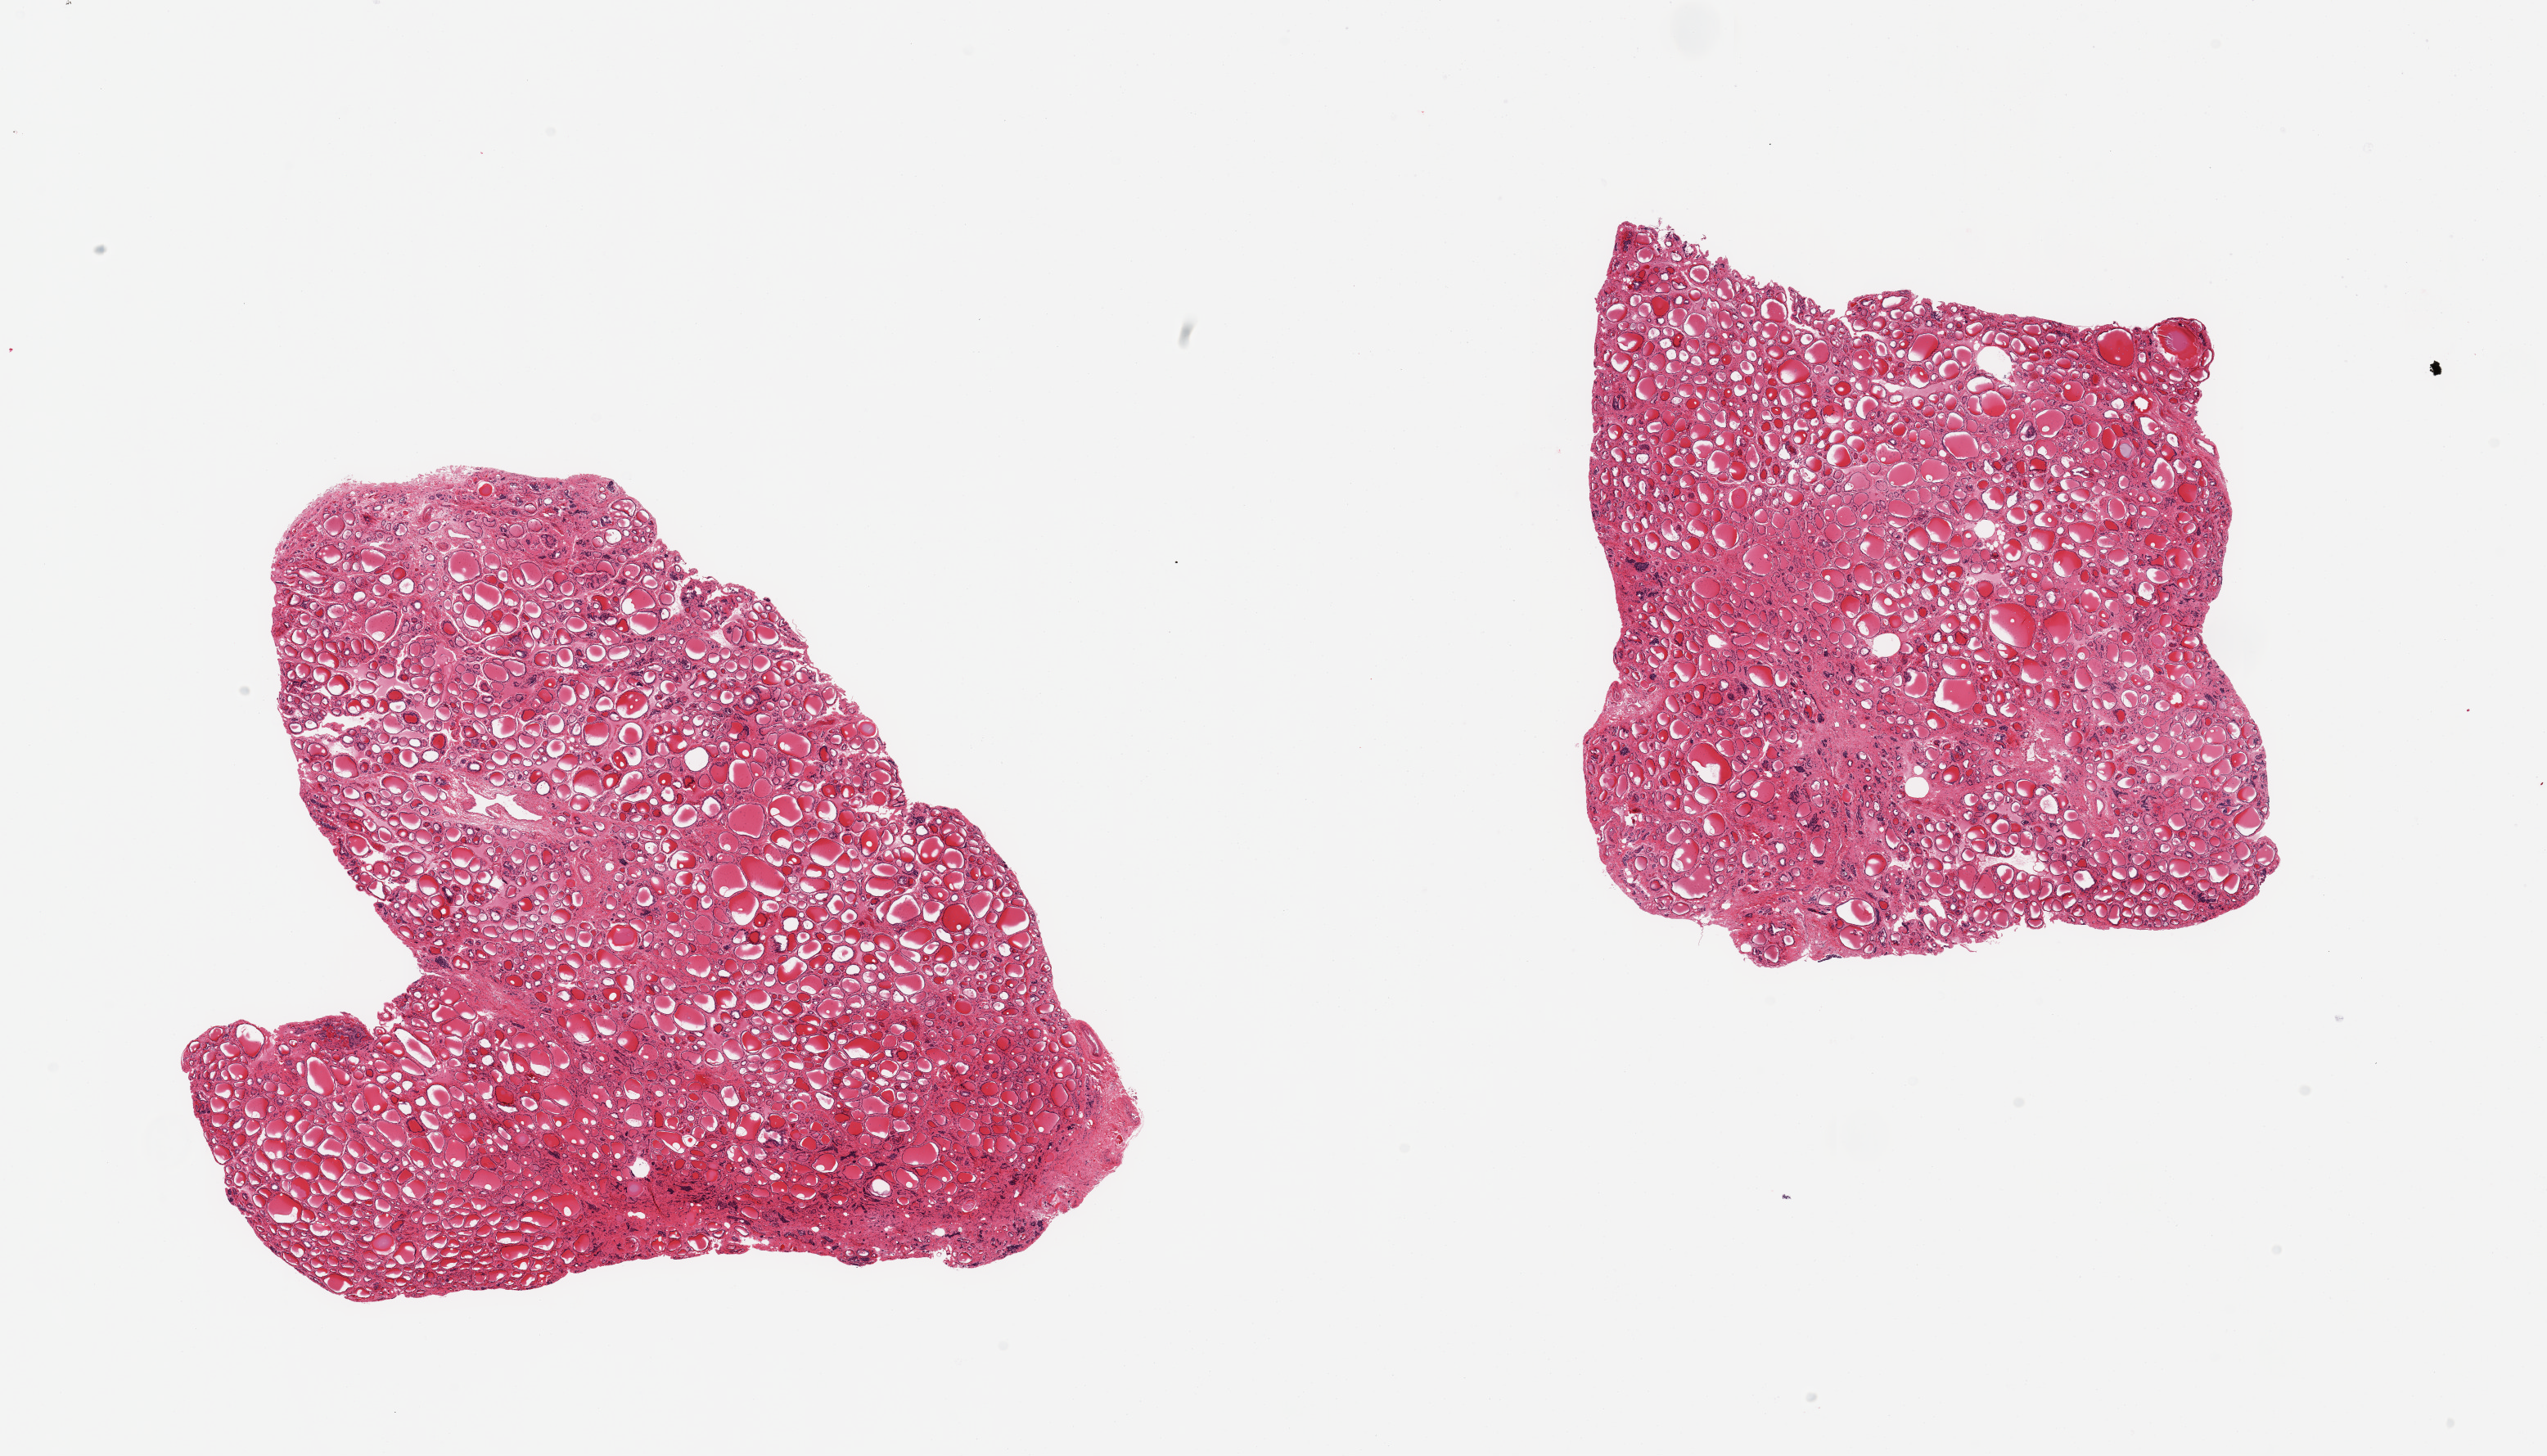
Digitized hematoxylin and eosin (H&E)-stained section — a low-resolution overview of the entire scanned area, about 24.6 x 14.1 mm (from a 20x scan); PAXgene-fixed, paraffin-embedded tissue; section of thyroid (target tissue); tissue donor sample. Donor: female.
* pathologist's review note for this sample: 2 pieces; focal fibrotic areas <10%